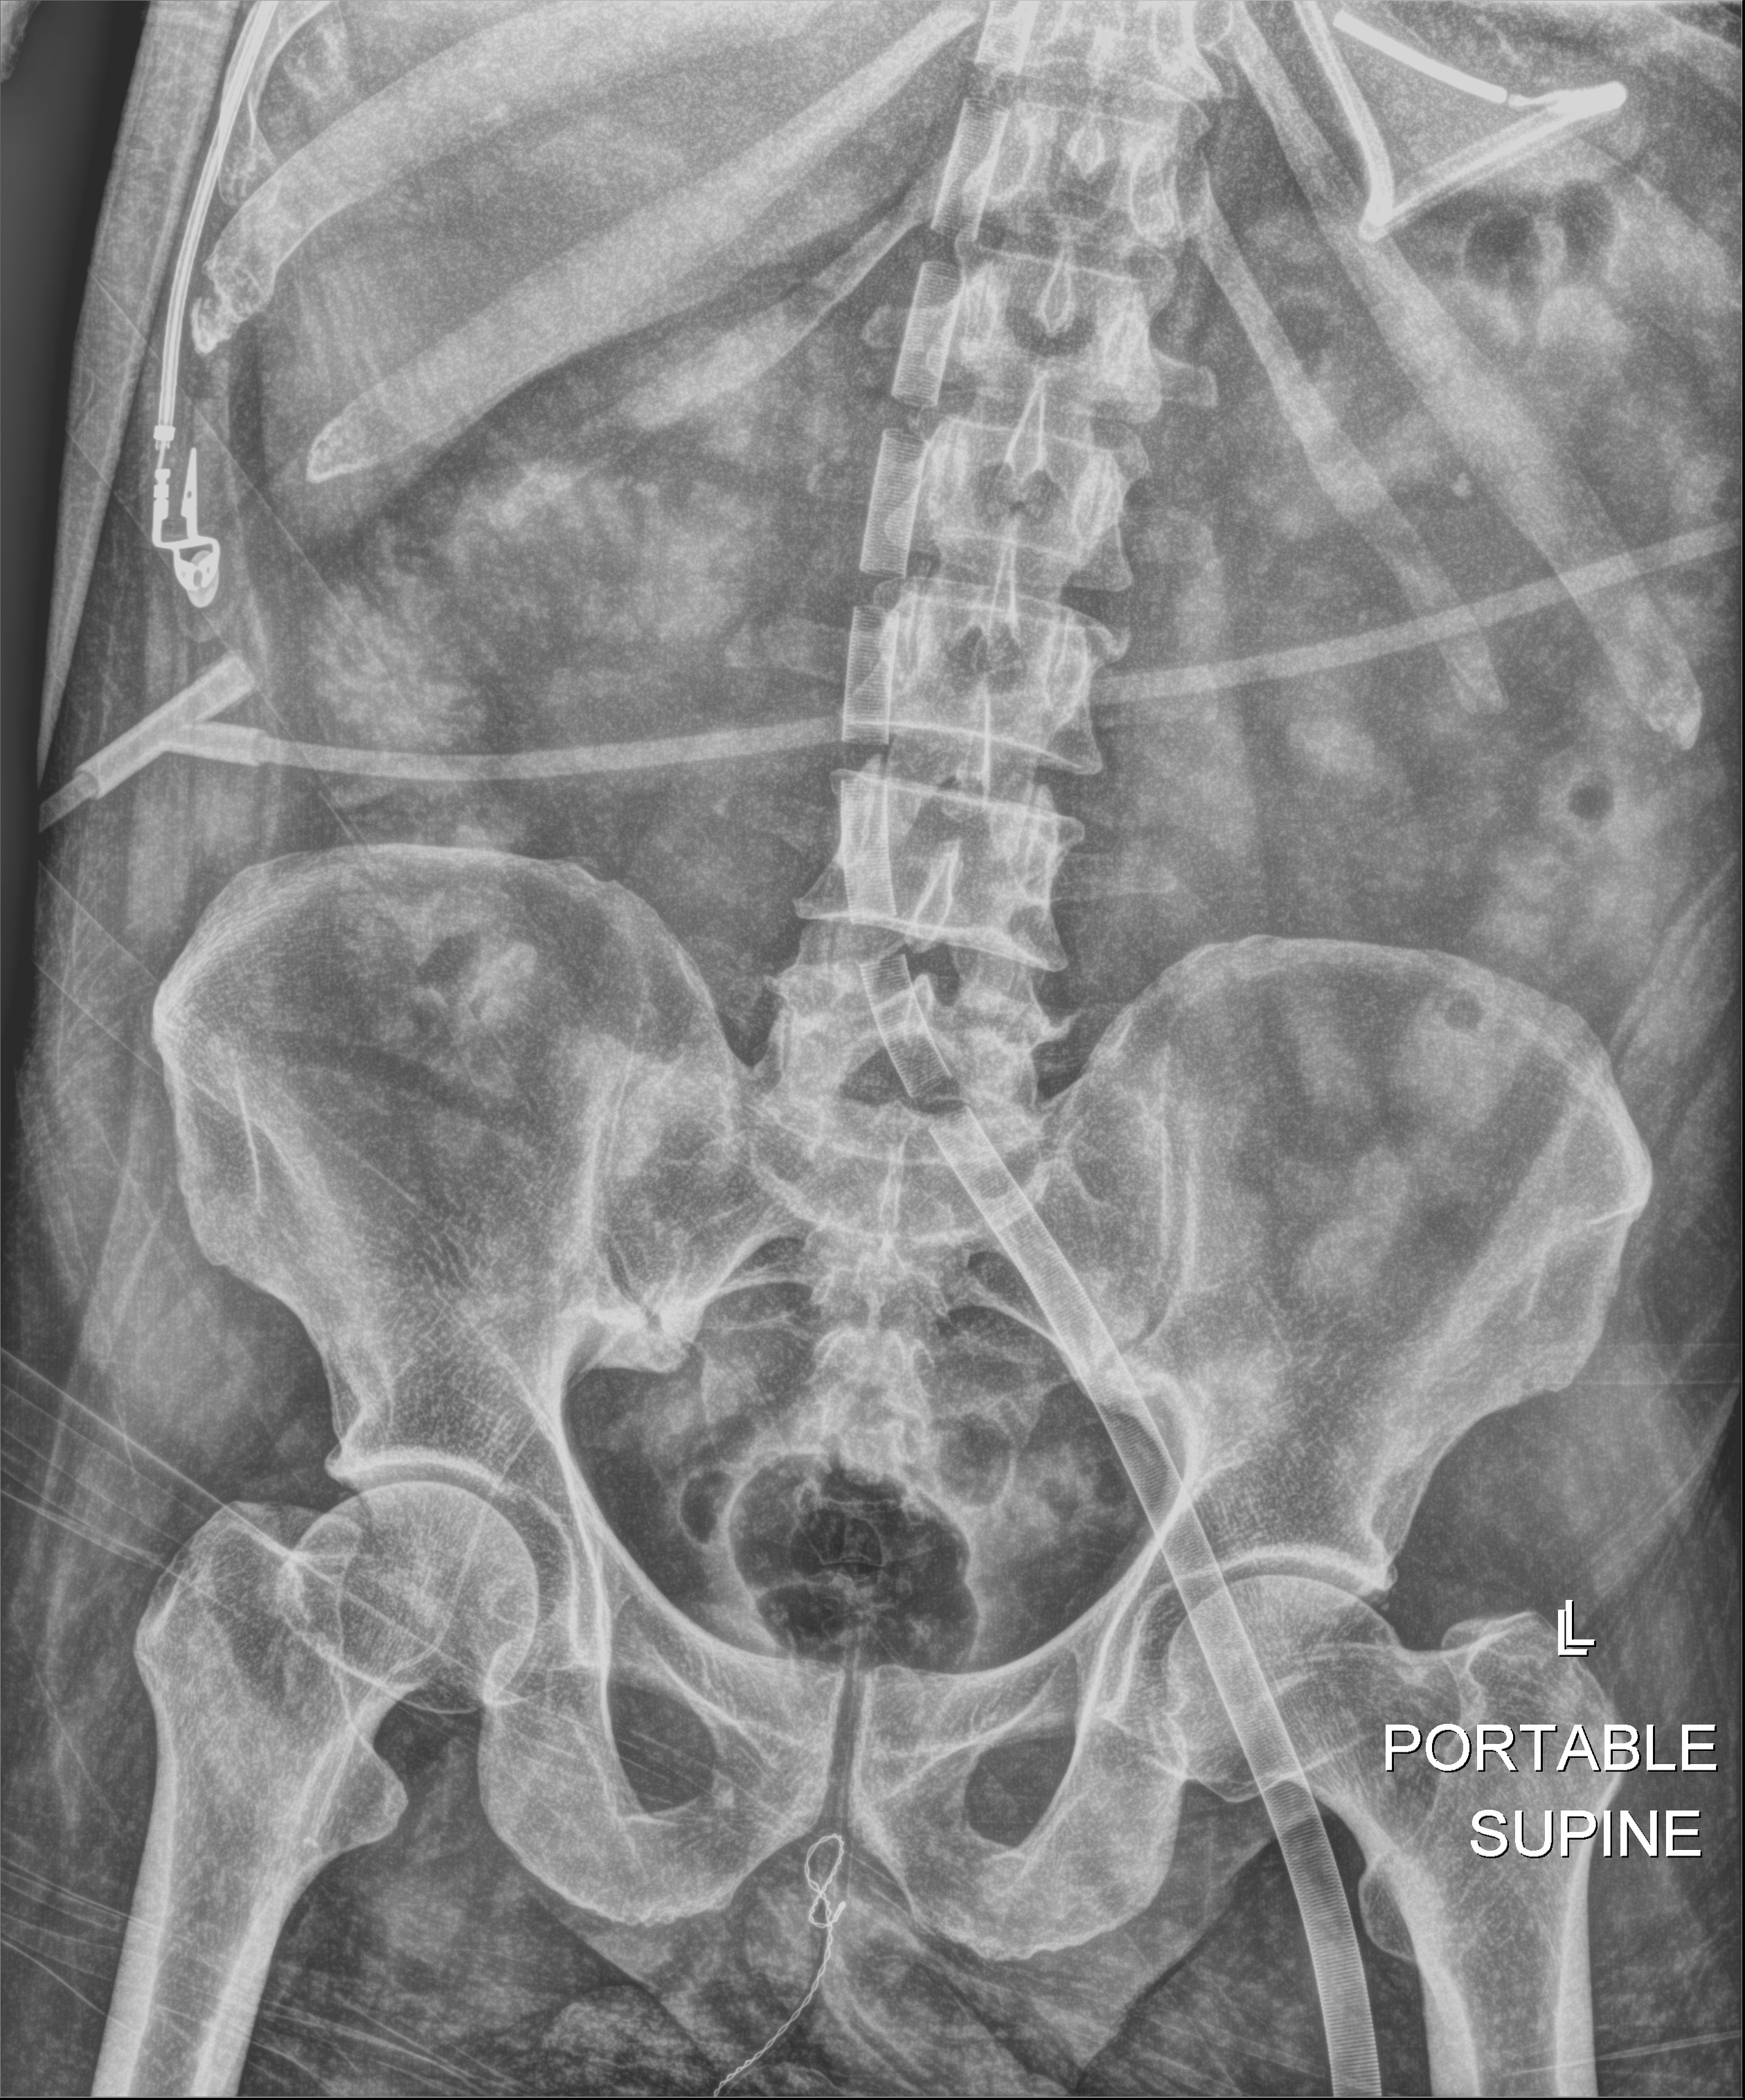
Portable abdomen radiograph, anteroposterior (AP) projection. Male patient hospitalised with COVID-19, age 18–59 years.
Admission-level facts for this patient (not findings on this image; timing relative to this image not recorded):
- mechanically ventilated during this hospital stay: yes